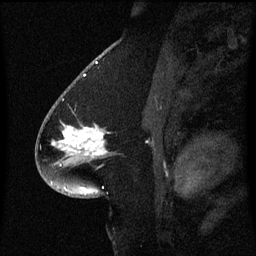
Breast MRI (dynamic contrast-enhanced), one sagittal slice. Dynamic contrast-enhanced series, image 2 of 3 at this slice position (ordered by acquisition). 1.5 T. TE 4.2 ms, TR 8.4 ms. 2 mm slice thickness. 256 × 256 image matrix, field of view 200 × 200 mm. Female patient, age 54 years. From the clinical record (not read from this slice): setting: breast cancer imaged before/during neoadjuvant chemotherapy; receptor status: HR-positive, HER2-negative.
Annotated regions visible in this slice (semi-automatic segmentation, software-assisted and operator-edited):
- analysis volume of interest (the breast-tissue region the enhancement analysis was run in; not a lesion): bounding box (x1, y1, x2, y2) in pixels: (46, 100, 112, 167)
- tumour enhancement mask (voxels above the 70 % enhancement threshold inside the analysis volume of interest): (53, 126, 105, 155)